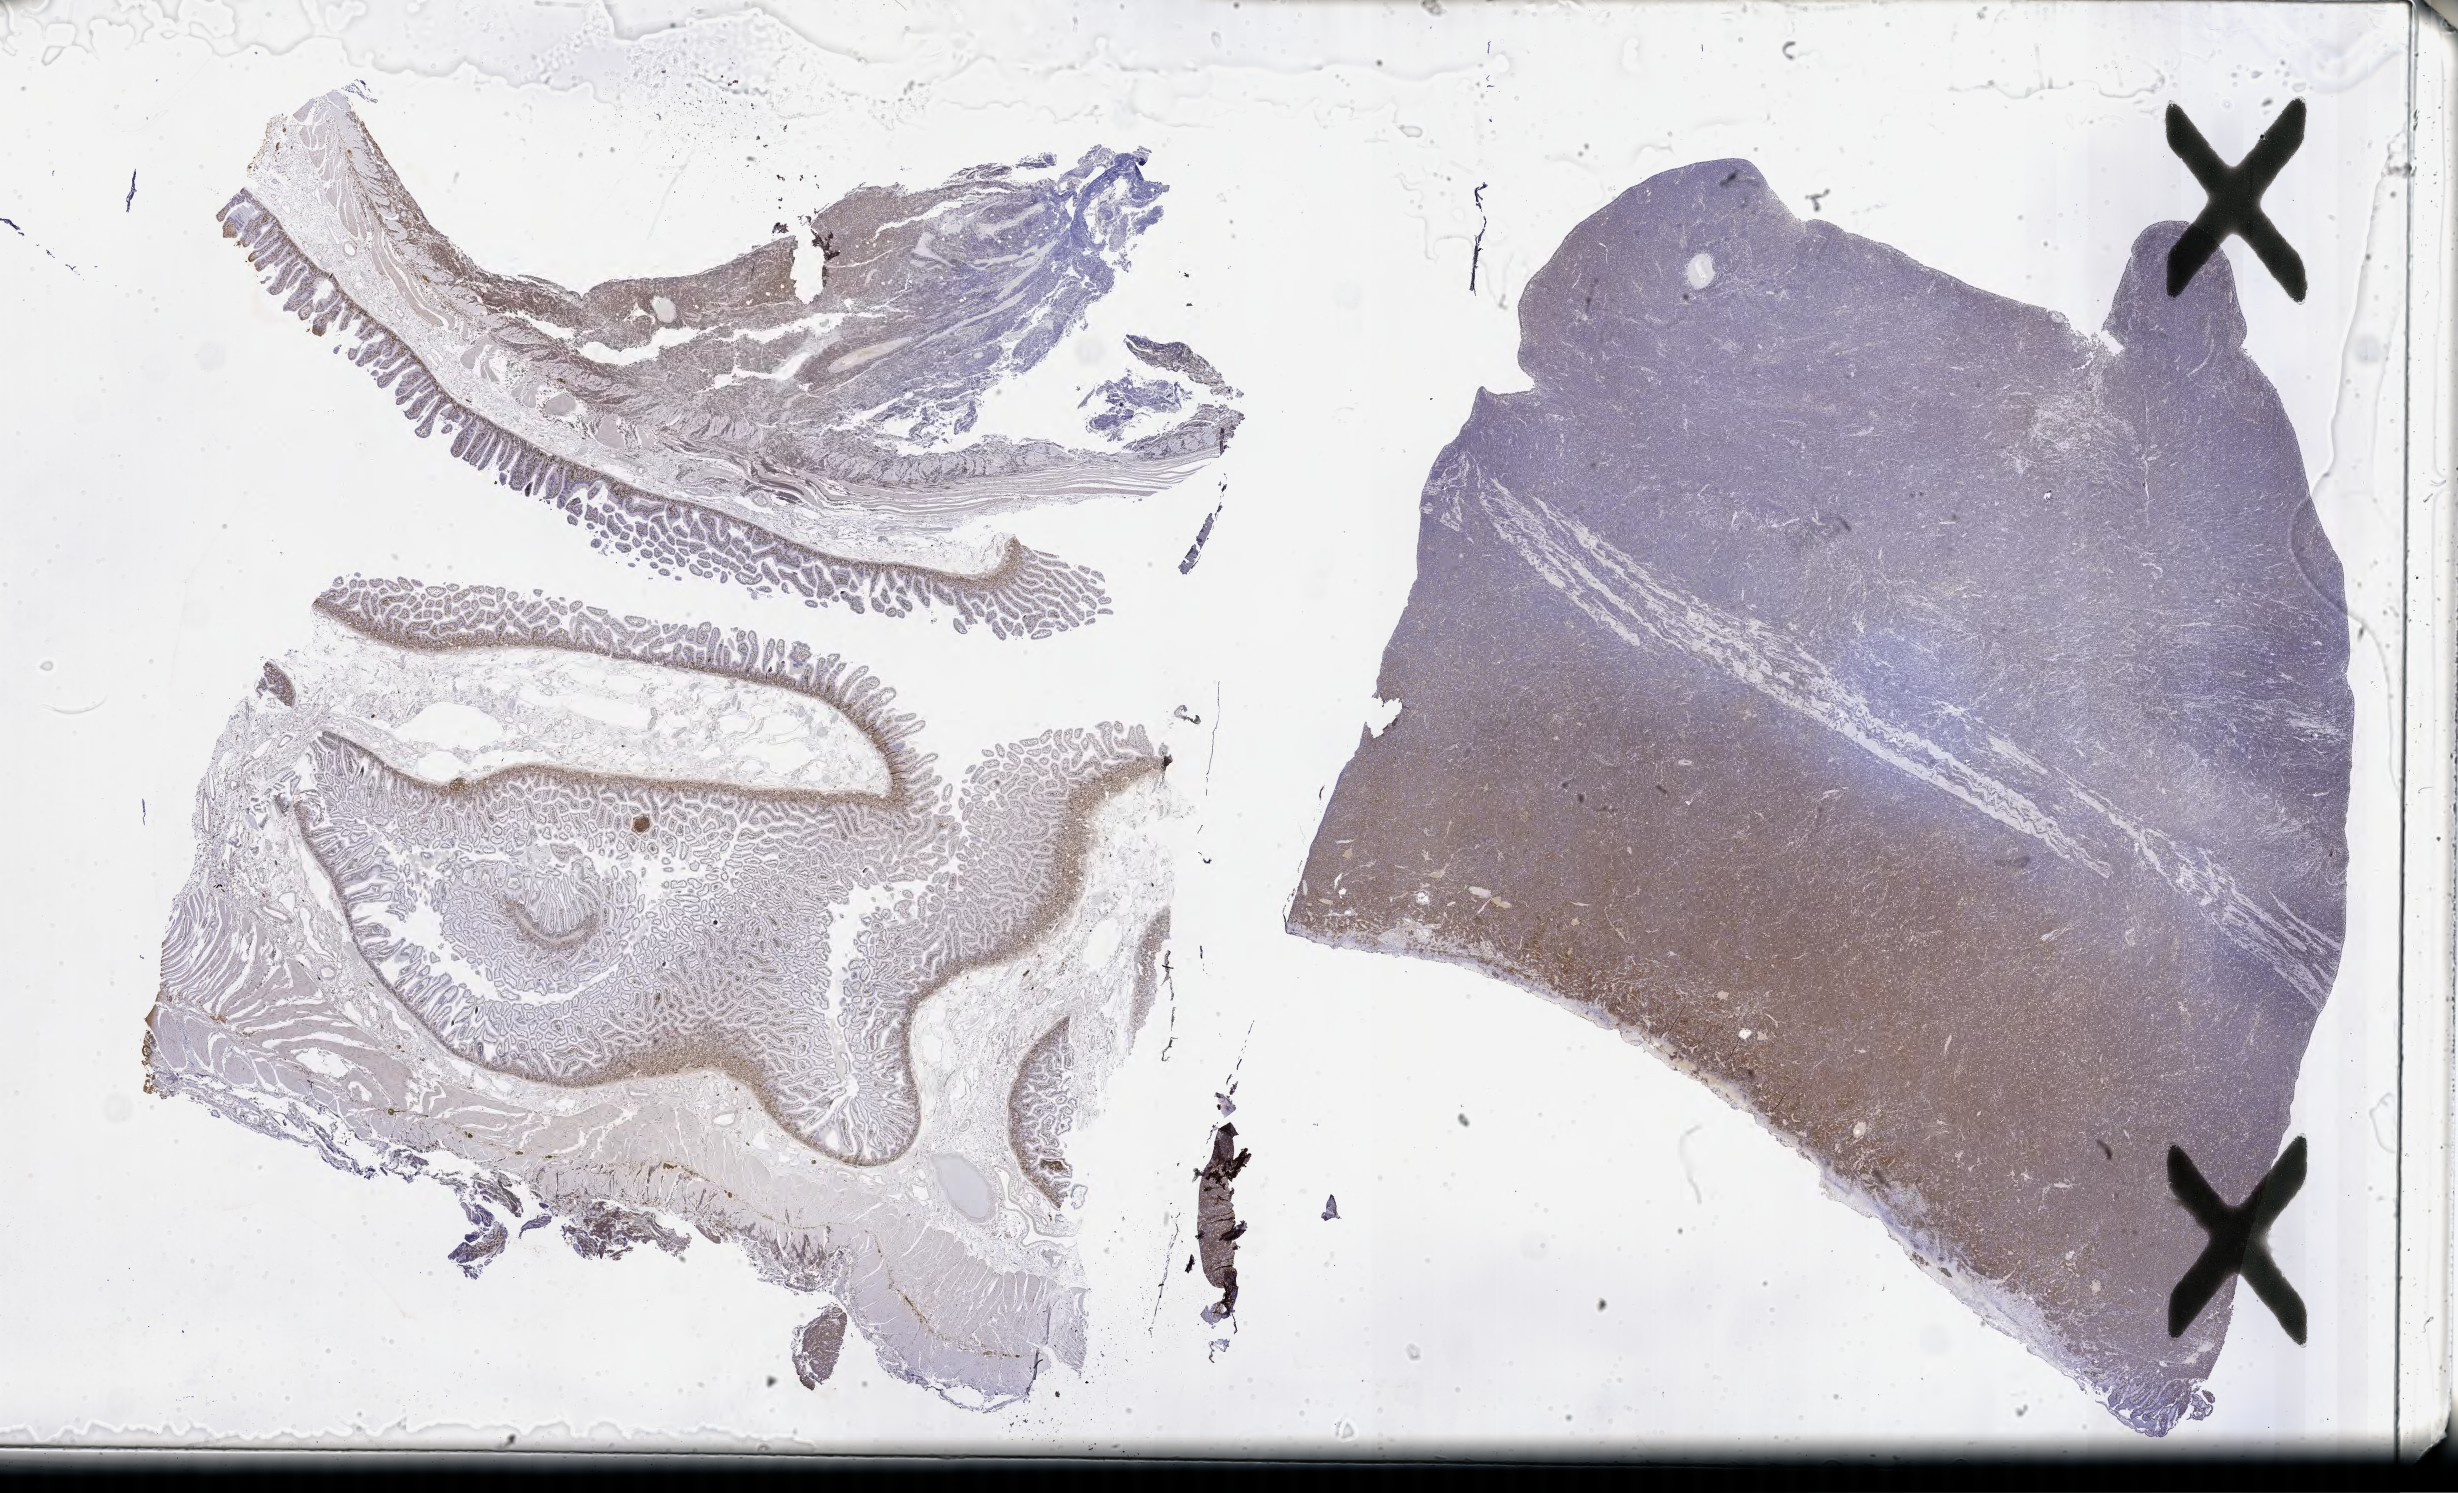
Immunohistochemistry (IHC) whole-slide image stained for BCL2 — low-resolution overview of the scanned area, about 39.7 x 24.1 mm, tumor tissue. Male patient, age 36 years.
- diagnosis: Burkitt lymphoma, NOS